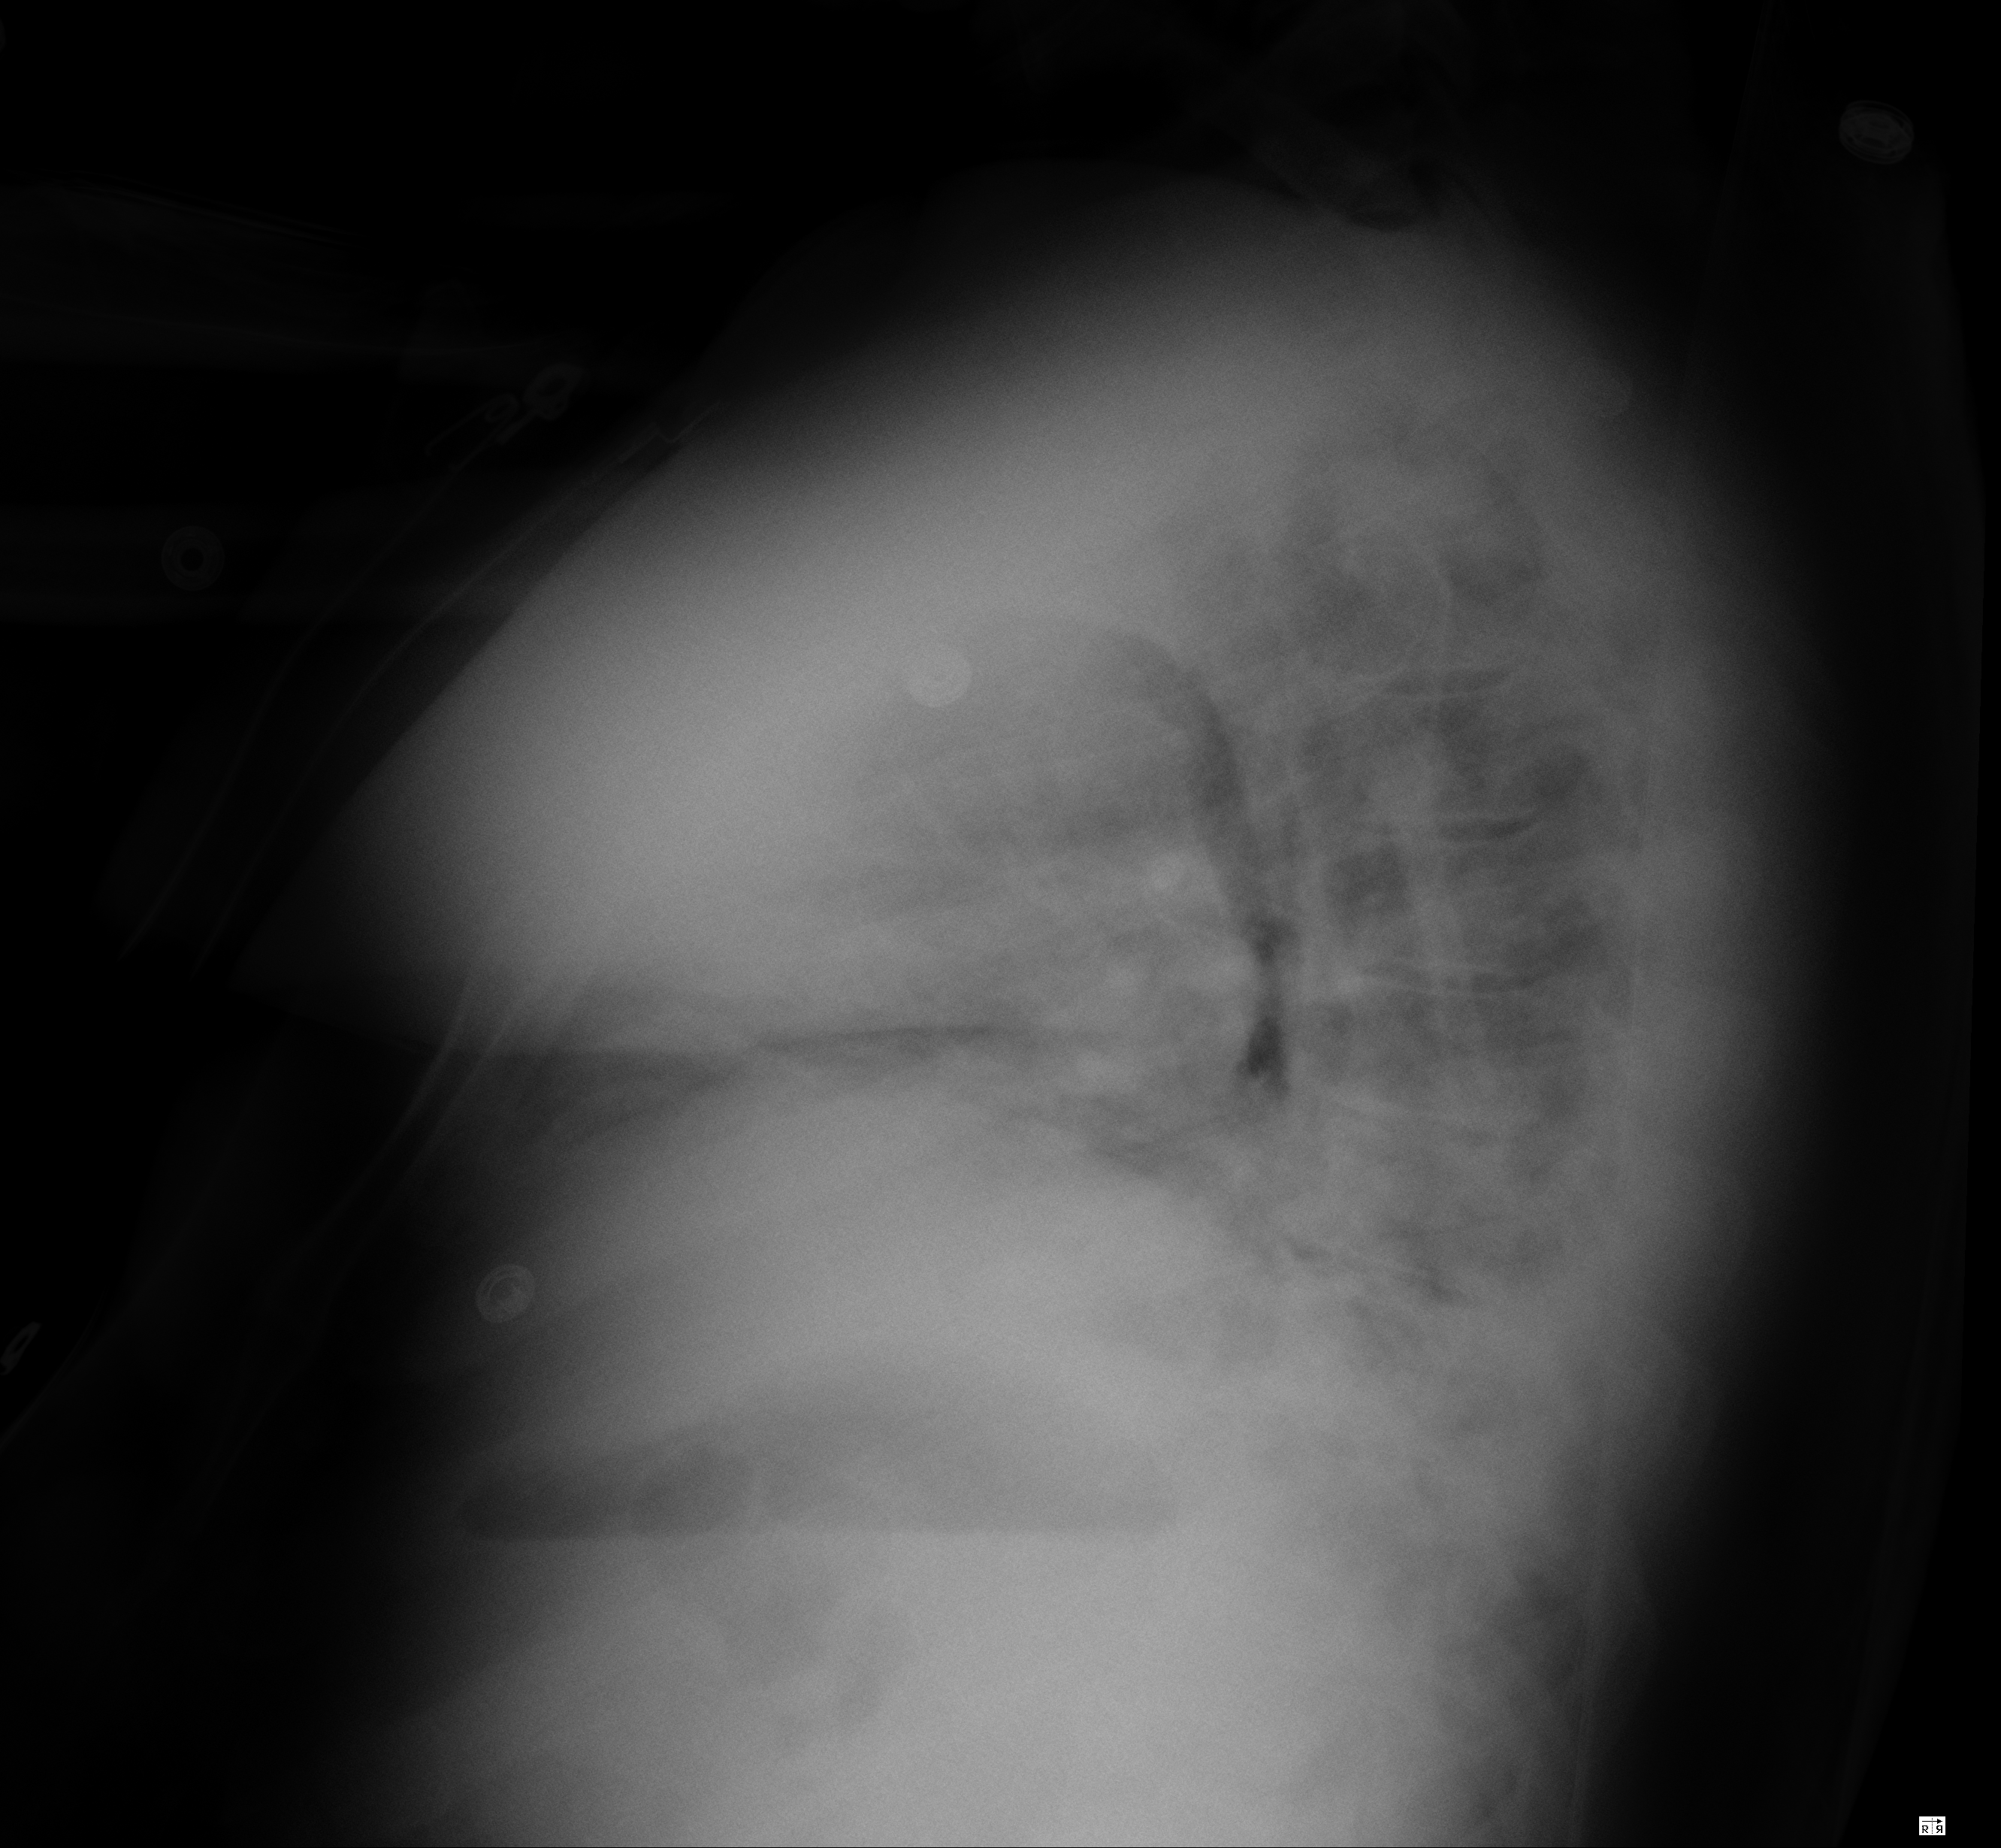
Chest radiograph, lateral projection. Male patient, age 44 years; imaged 0 days after the COVID-19 diagnosis.
Radiologist key findings (as recorded): patchy increased opacity in the lower lobes bilaterally, more pronounced on the lateral view. Small pleural effusions.